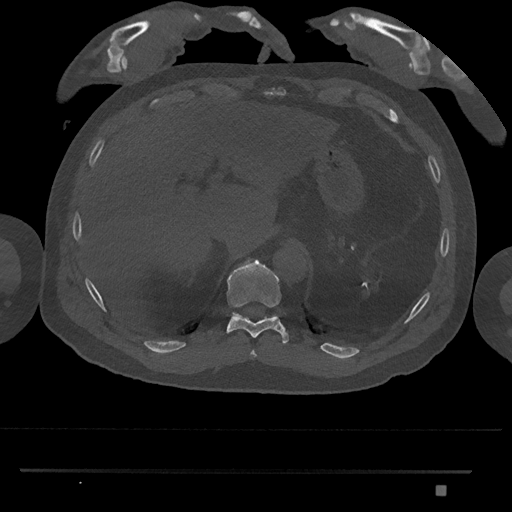
CT including the spine, one axial slice. Slice 995 of 1134 in the series (ordered by position). Reconstruction kernel Br40s/3. 120 kVp. Bone window (W 1800 / L 400 HU). 0.5 mm slice thickness. 512 × 512 image matrix. Patient: male, 65 years. From the clinical record (not read from this slice): primary cancer: prostate.
Structures marked on this image (semi-automatic segmentation, software-assisted and operator-edited):
- T10 vertebra: bounding box [x1, y1, x2, y2] px = [227, 259, 289, 344]
- T11 vertebra: [232, 312, 276, 318]
- T9 vertebra: [250, 350, 256, 359]